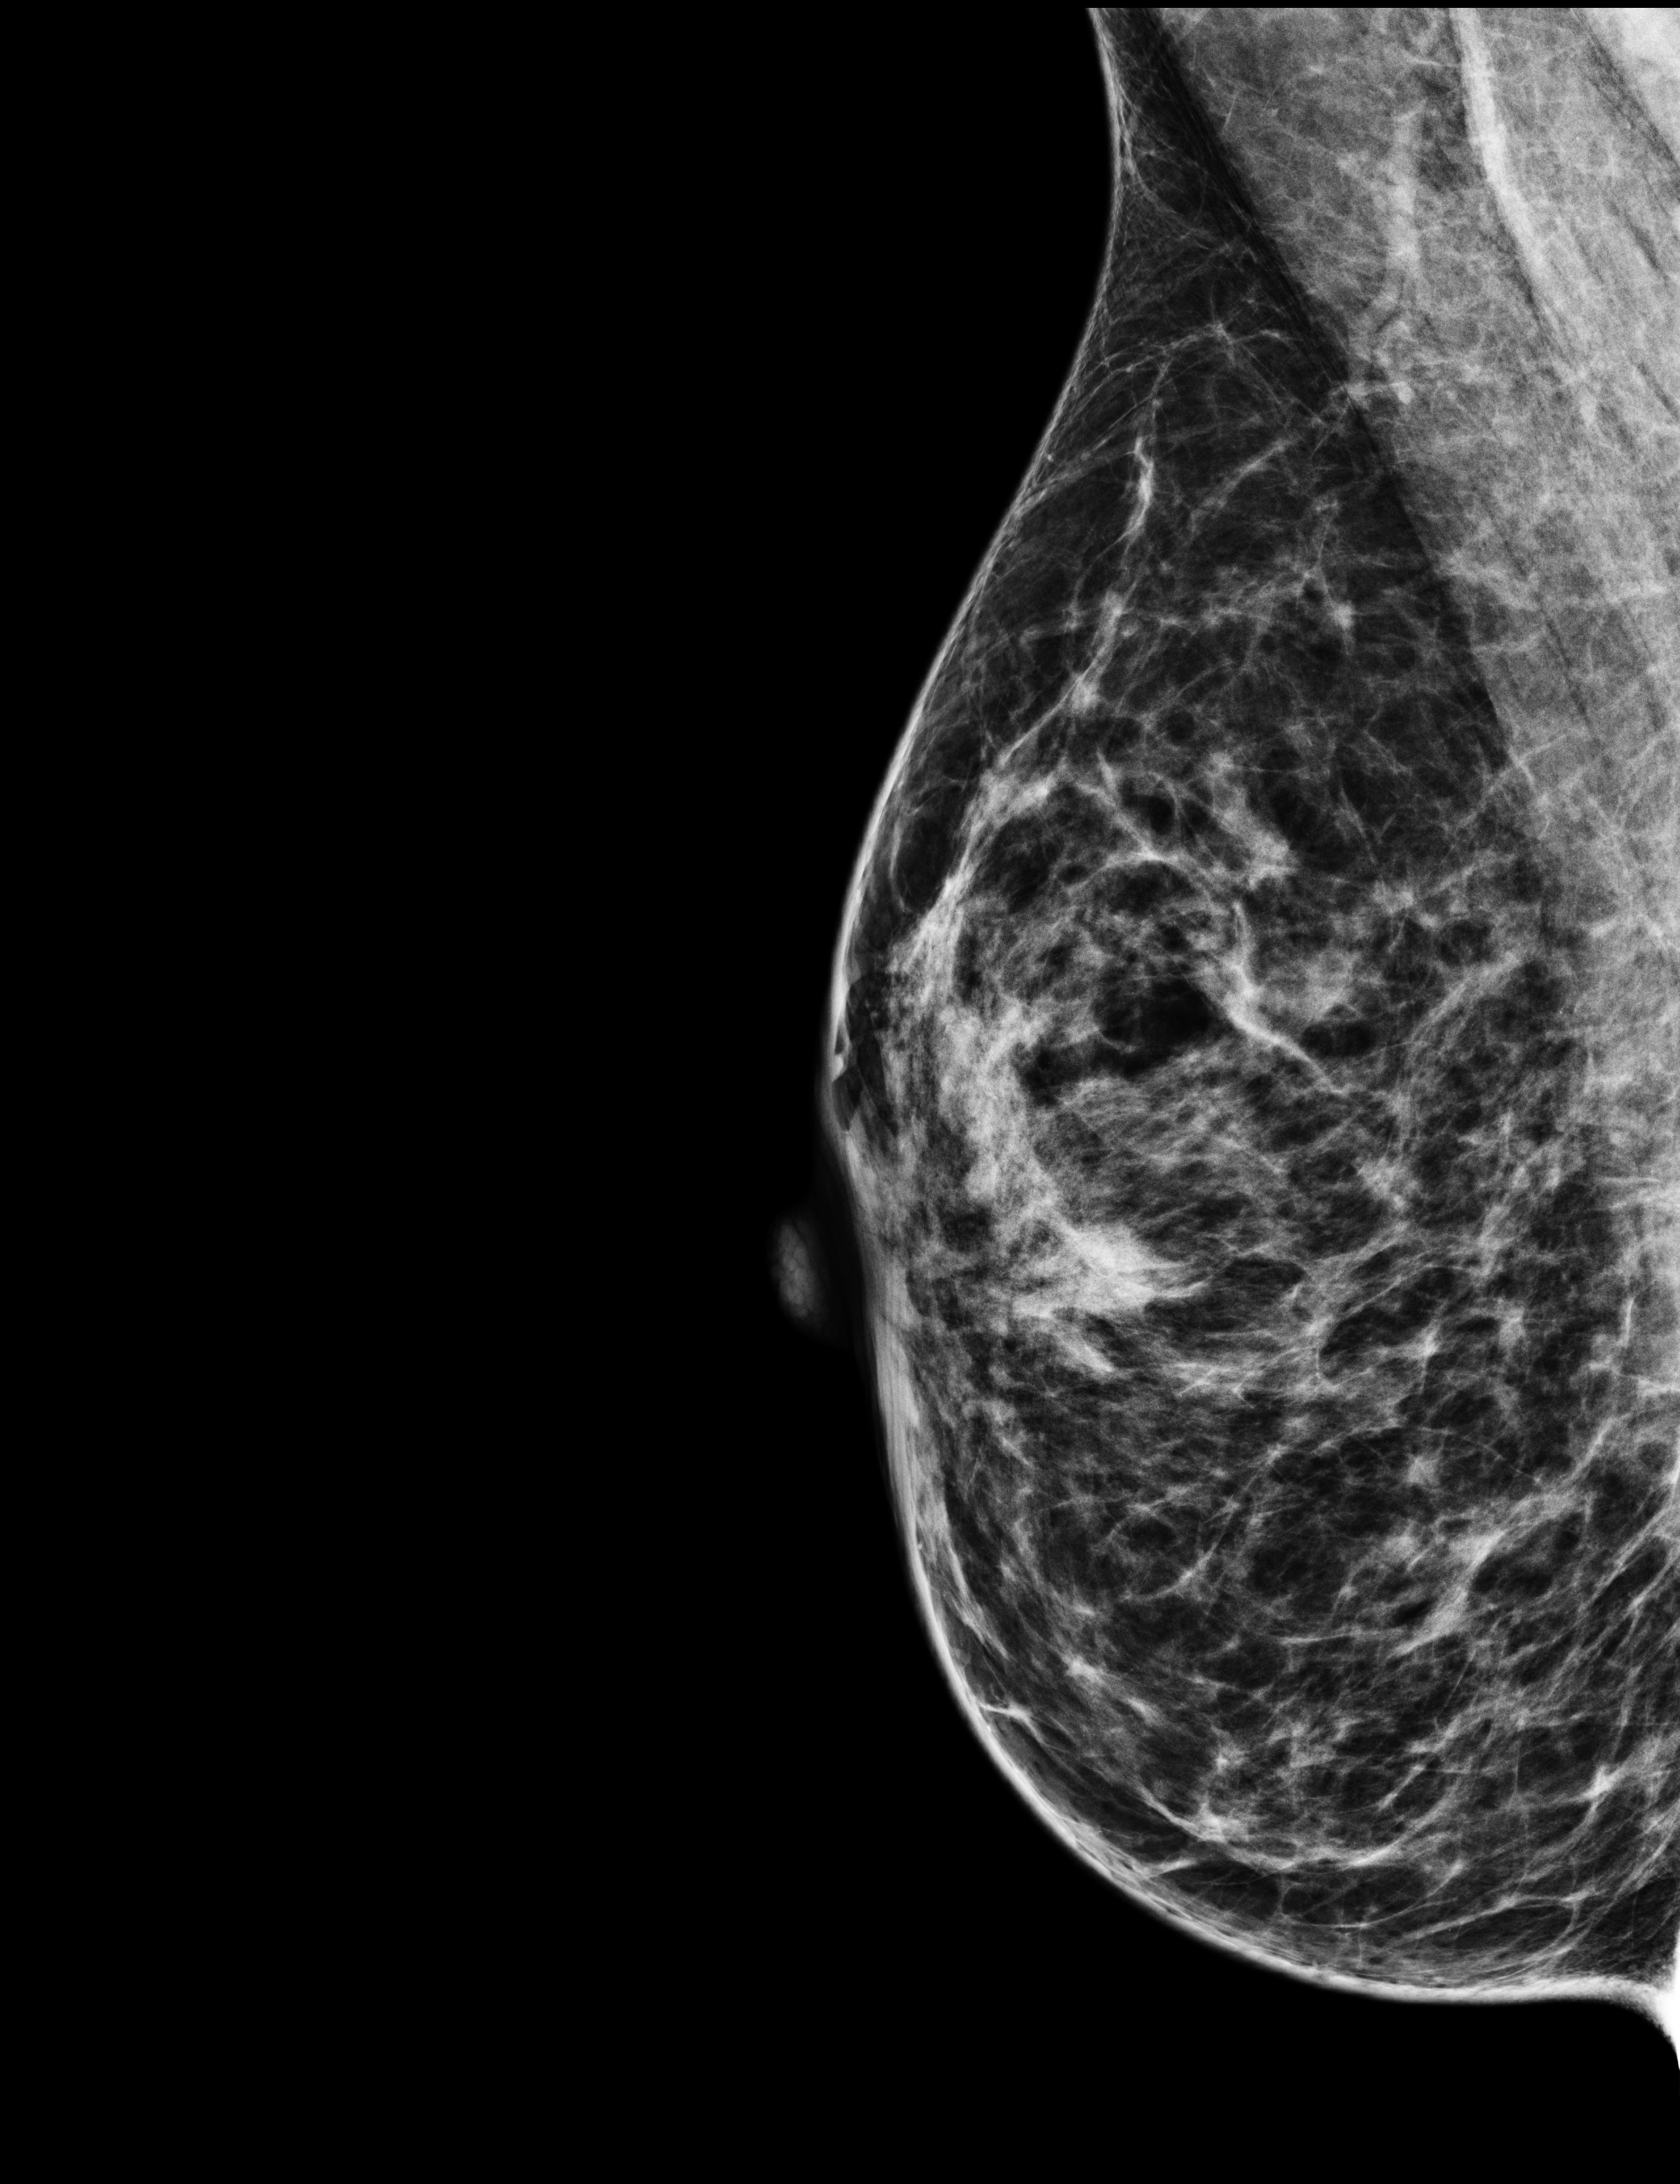
Annual screening mammography examination. Patient: female, 44 years.
Image type: full-field digital mammogram. Breast: right. Projection: mediolateral oblique (MLO) view.